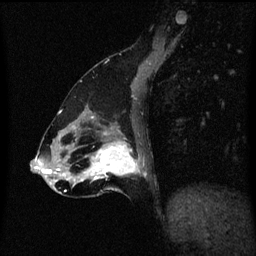
Breast MRI (dynamic contrast-enhanced), one sagittal slice; slice 24 of 60 in the series (ordered by position); dynamic contrast-enhanced series, image 2 of 3 at this slice position (ordered by acquisition); 1.5 T; TE 4.2 ms, TR 8.4 ms; 2 mm slice thickness; 256 × 256 image matrix, field of view 200 × 200 mm. Patient: female, 47 years.
Outlined on this slice (semi-automatic segmentation, software-assisted and operator-edited):
- analysis volume of interest (the breast-tissue region the enhancement analysis was run in; not a lesion): bounding box [x1, y1, x2, y2] px = [85, 136, 142, 197]
- tumour enhancement mask (voxels above the 70 % enhancement threshold inside the analysis volume of interest): [85, 142, 140, 181]